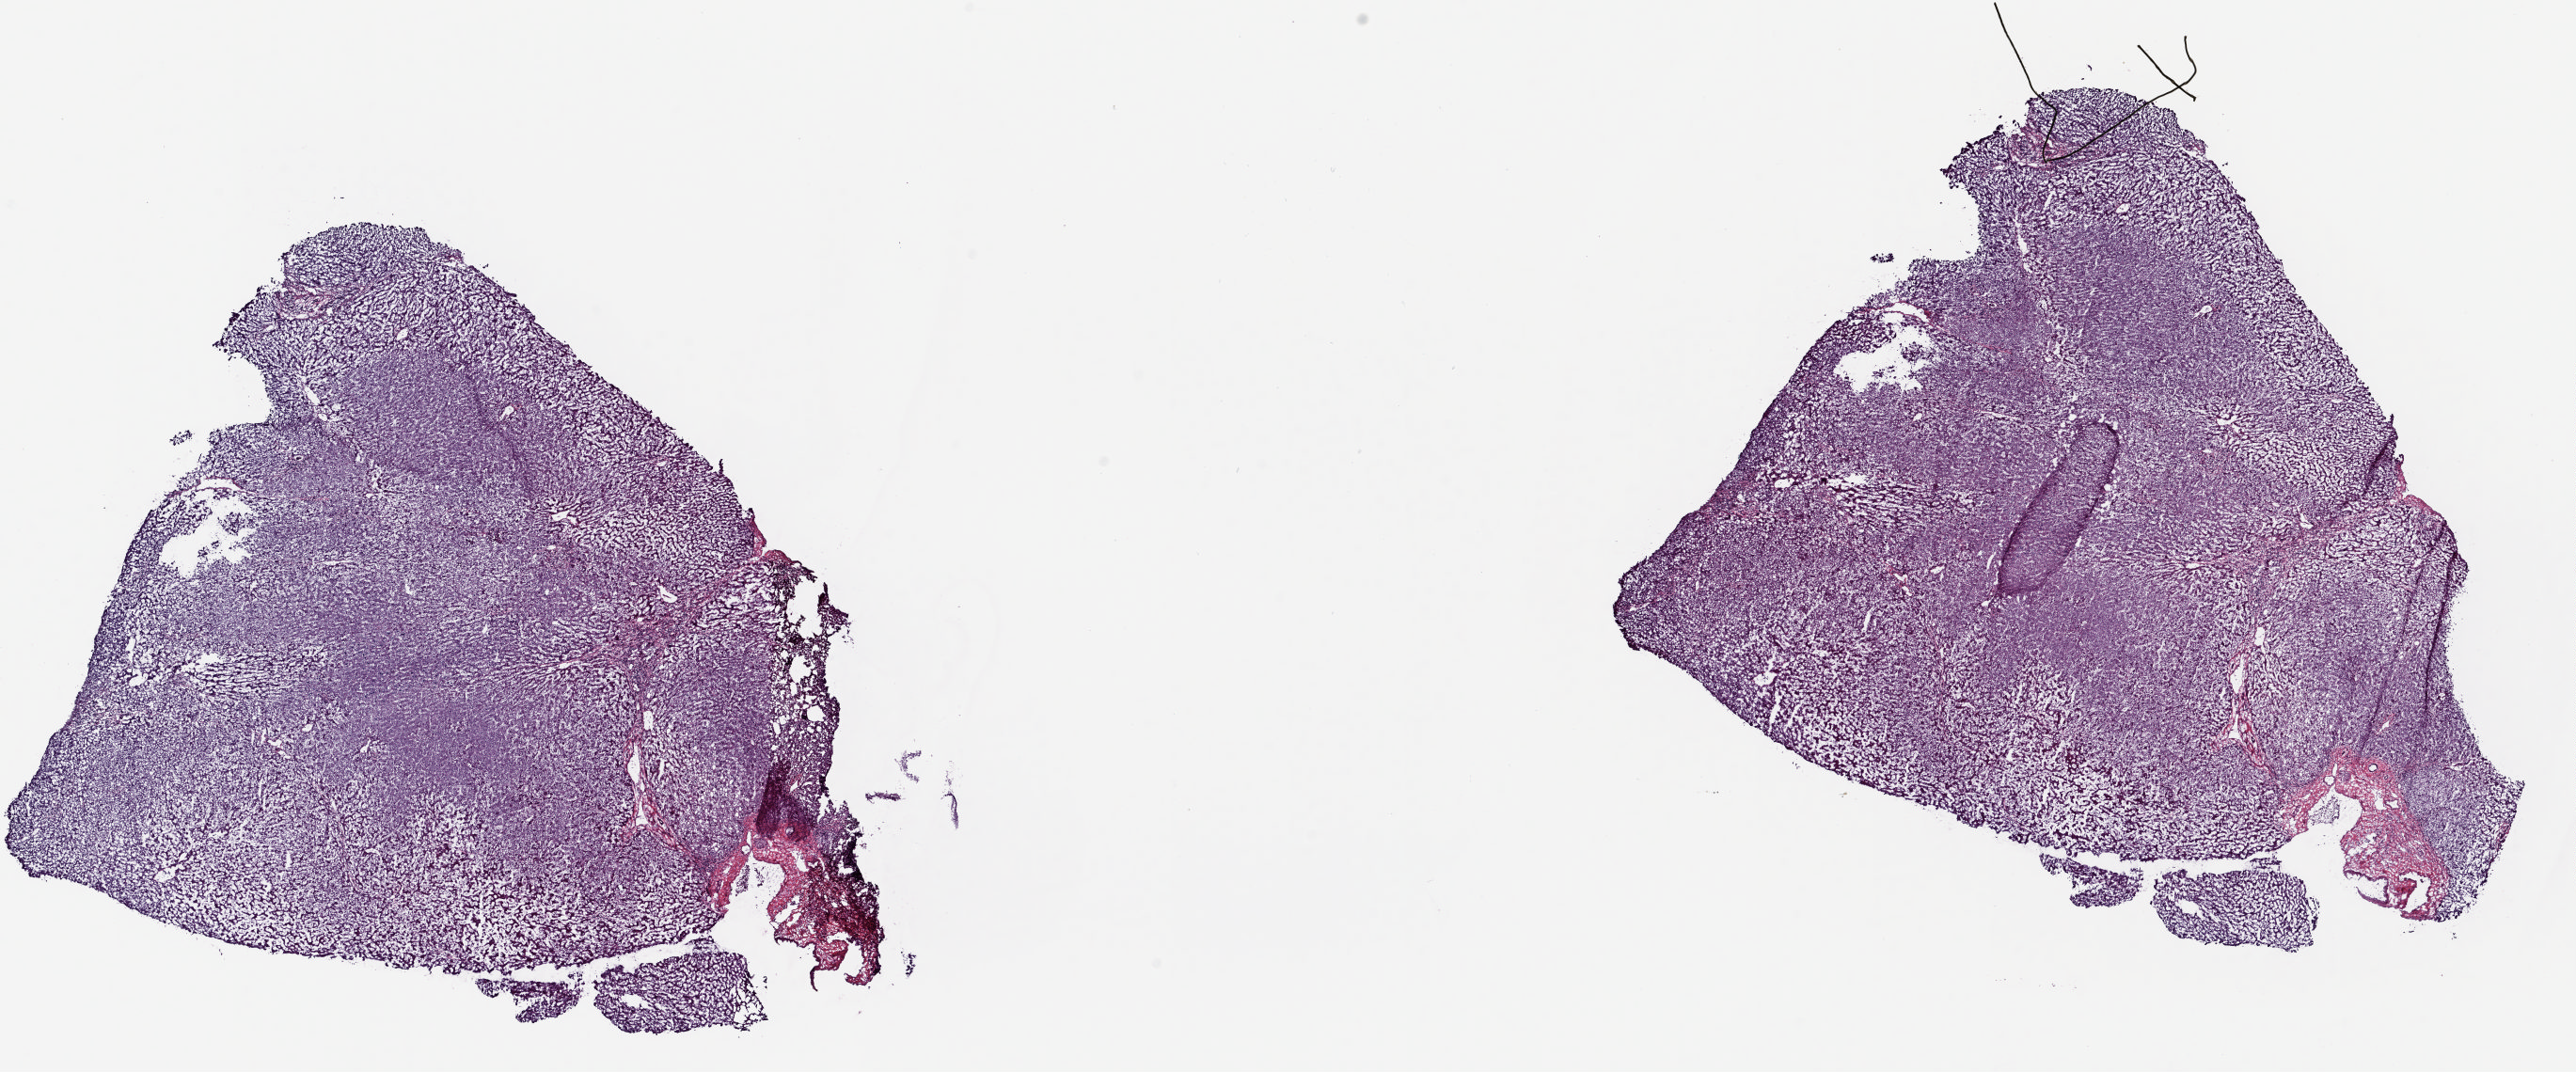
H&E whole-slide image, low-resolution overview of the scanned area, about 21.8 x 9.1 mm; frozen section from the top of the tissue portion; sample: solid tissue normal (non-tumour tissue), liver. Male patient; age at initial diagnosis 50 years. Composition of this section per pathologist review: tumour cells 0%, tumour nuclei 0%, normal cells 80%, stromal cells 20%, necrosis 0%. Inflammatory infiltration, as recorded: lymphocyte infiltration 5%, monocyte infiltration 0%, neutrophil infiltration 0%.
This section: solid tissue normal sample (biorepository sample class). Patient diagnosis: Hepatocellular carcinoma, NOS.